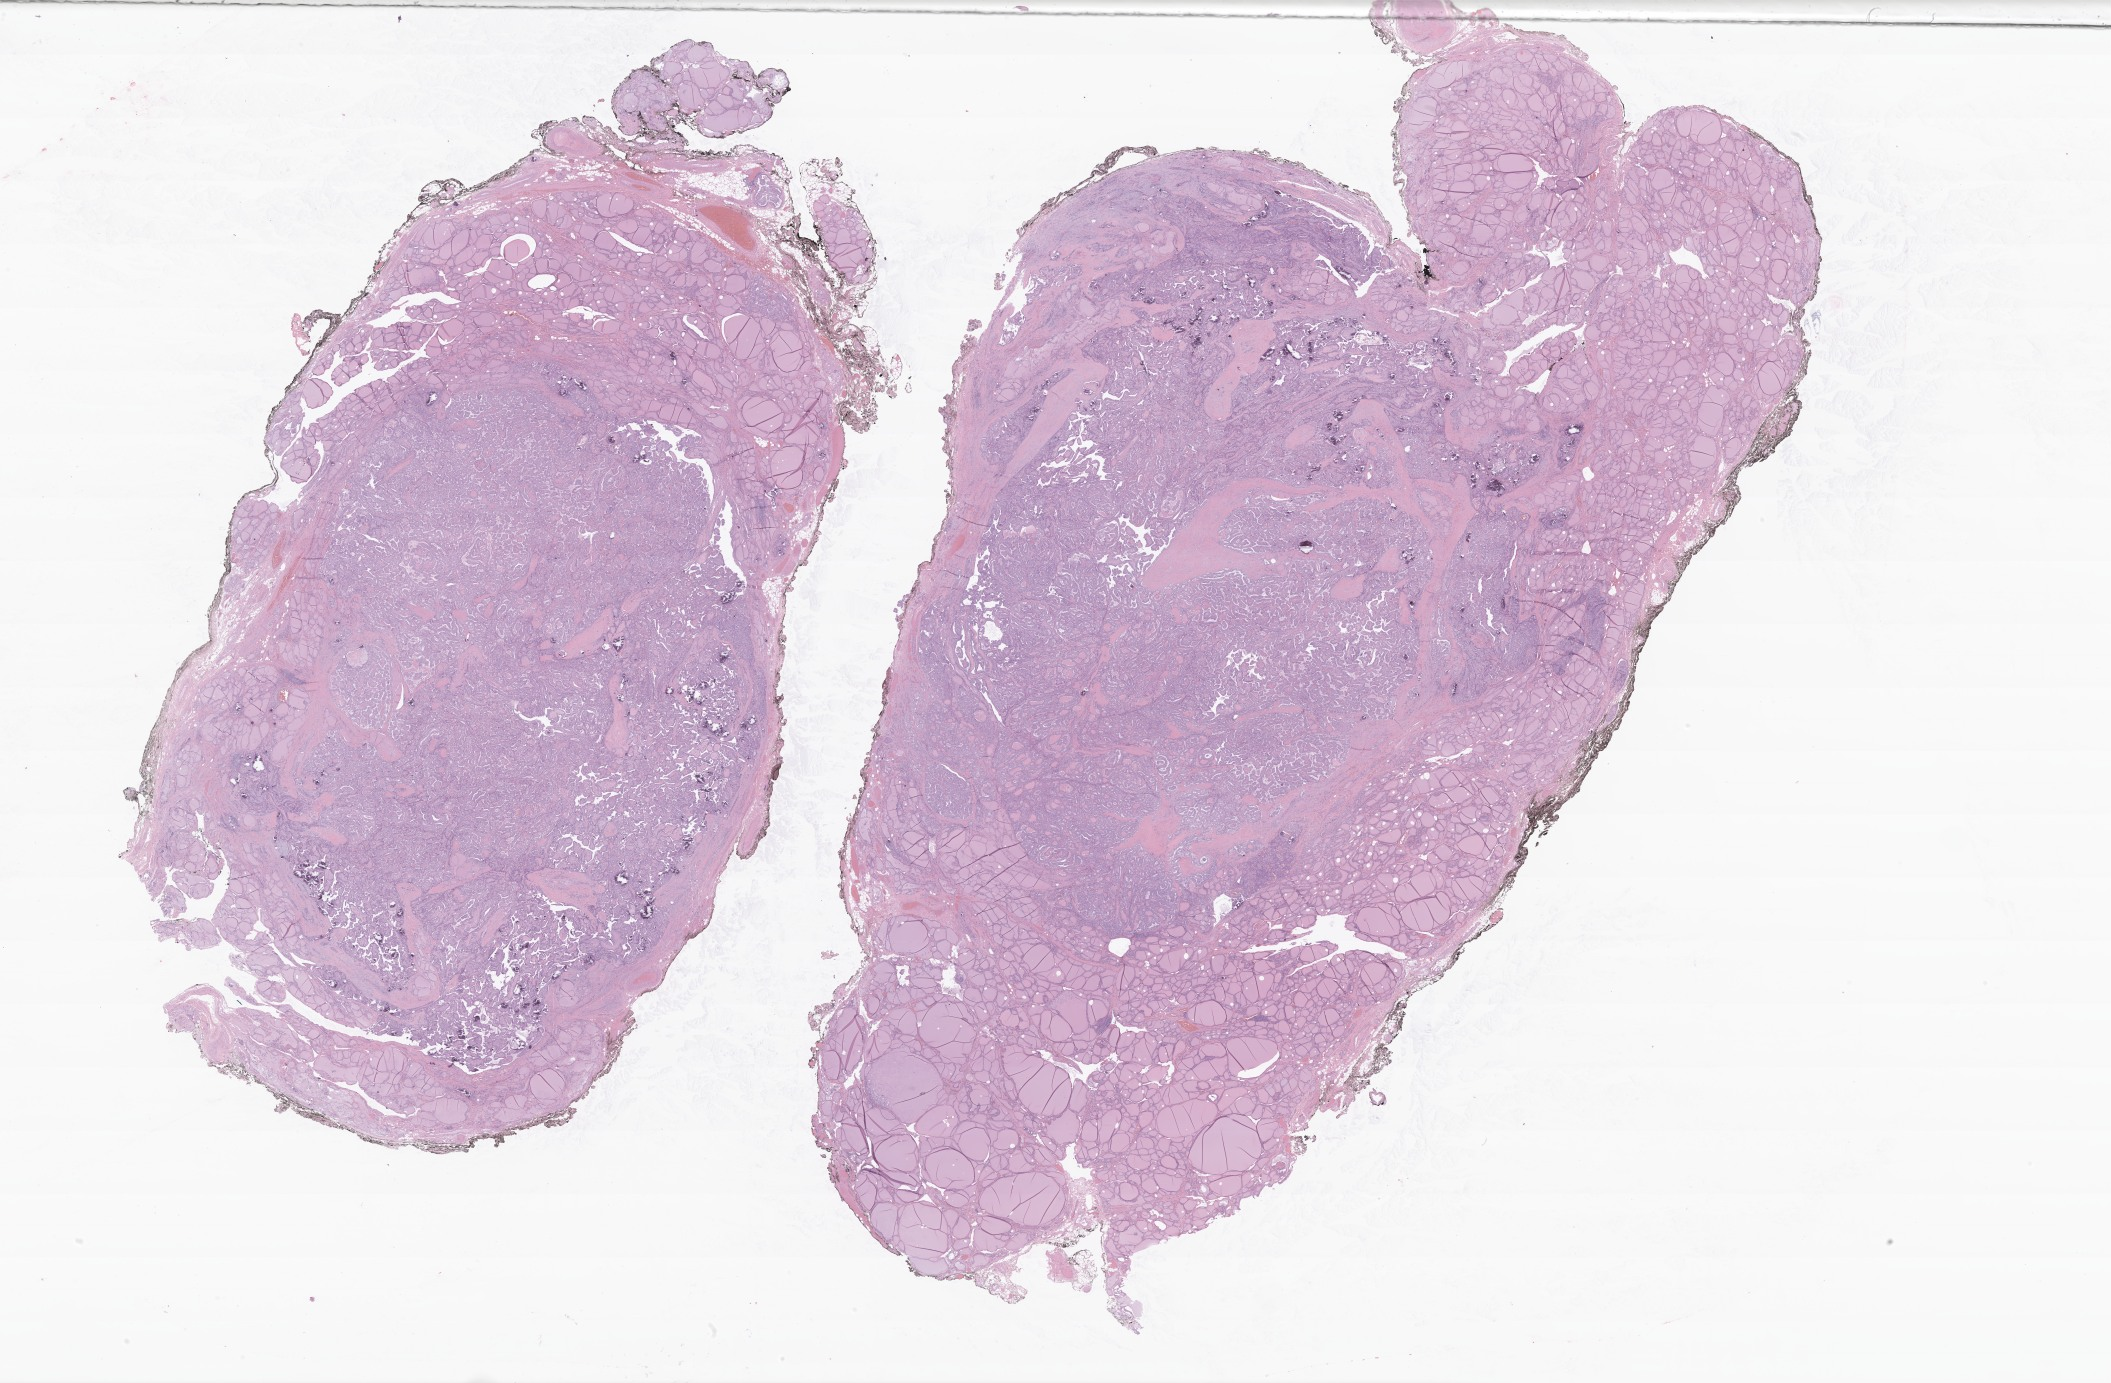
Digitized haematoxylin and eosin-stained section of tumor tissue from the thyroid — a low-resolution overview of the entire scanned area, about 35.5 x 23.3 mm. Formalin-fixed, paraffin-embedded (FFPE) tissue. Patient female; age 177 months (14 years 9 months).
Diagnosis: Papillary microcarcinoma.